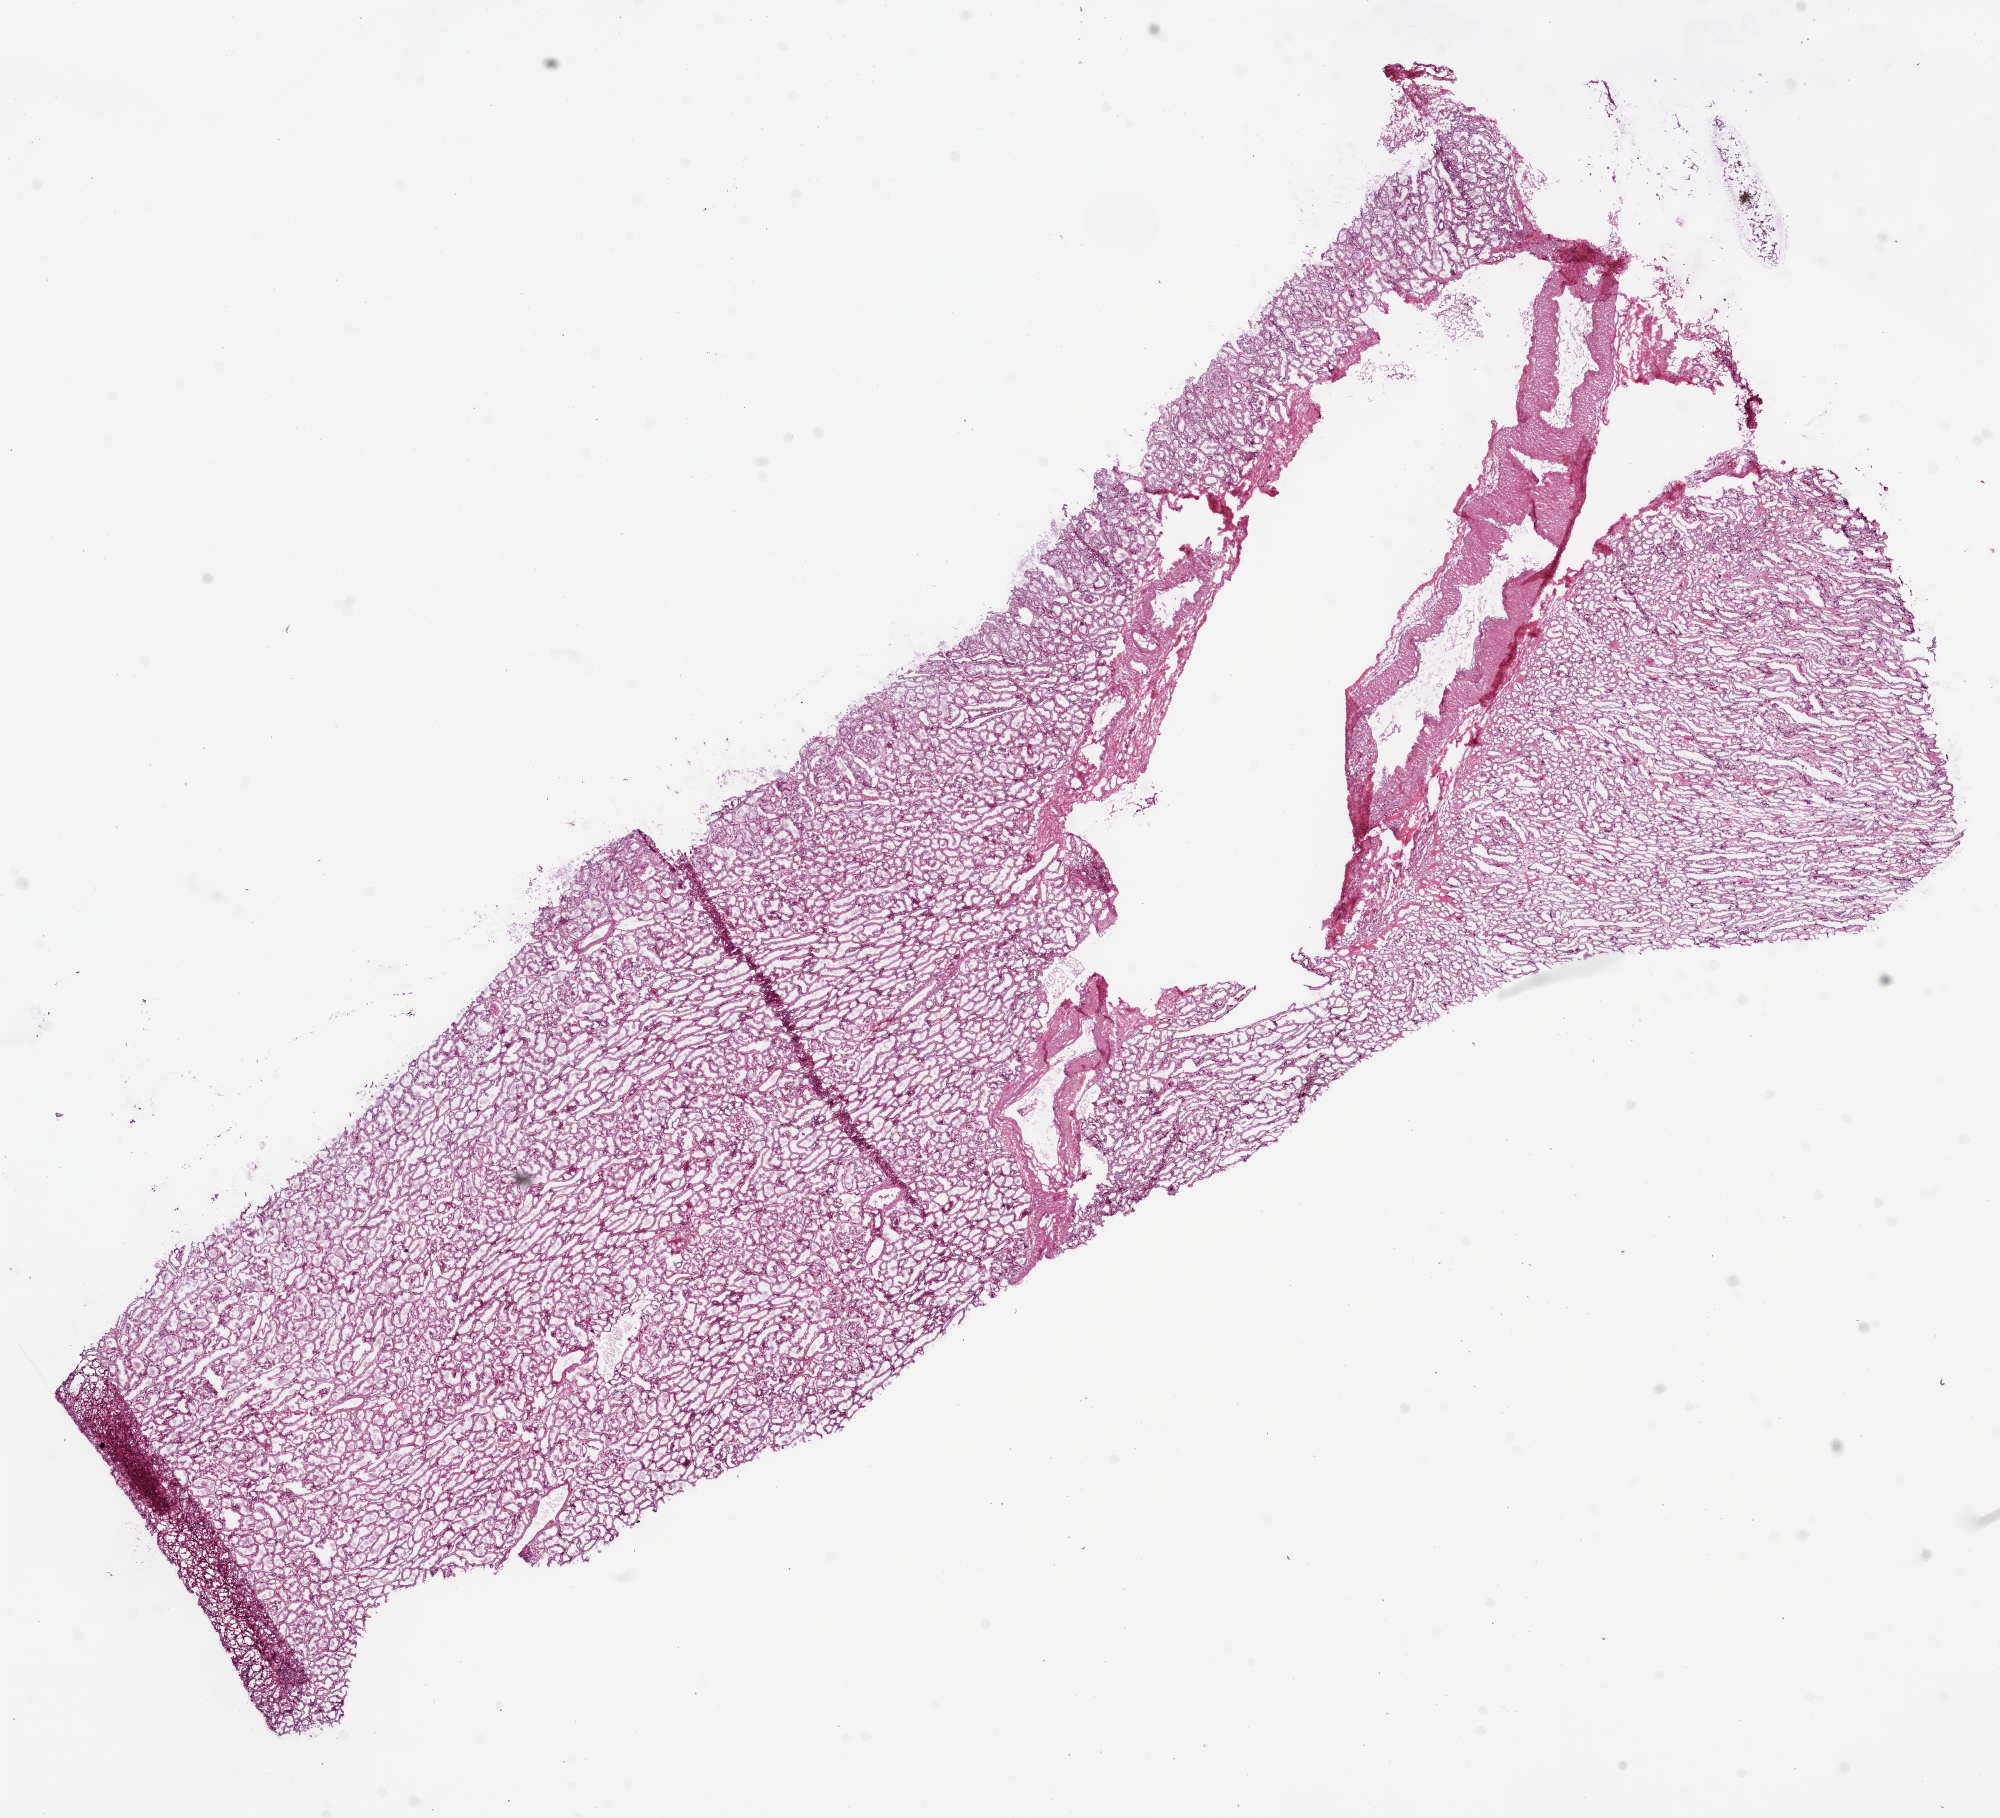
Digitized H&E-stained tissue section (whole slide) — whole scanned area (about 16.0 x 14.6 mm) shown as a low-resolution overview, frozen section from the bottom of the tissue portion, kidney, solid tissue normal (non-tumour tissue) sample. Male, age 78 years at initial diagnosis.
This section: solid tissue normal sample (biorepository sample class). Patient diagnosis: Clear cell adenocarcinoma, NOS.